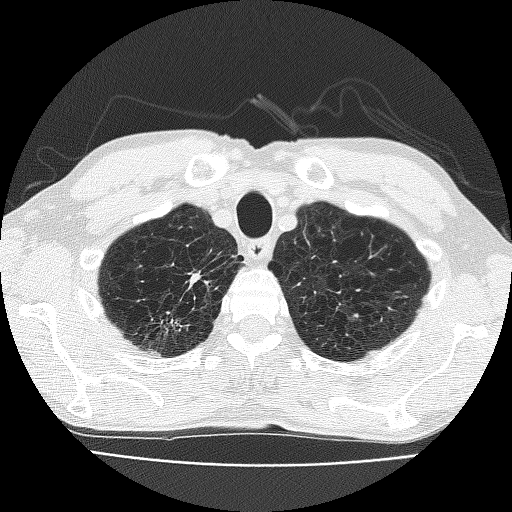
Chest CT (low-dose screening protocol), one axial image, third screening round (two years after baseline), lung window (W 1500 / L -600 HU), 2 mm slice thickness, lung (sharp) reconstruction kernel (FC51), 120 kVp, slice 33 of 185 in the series. Male participant, aged 63 years at enrolment.
• Lesion marked by an expert reader, bounding box <141,255,221,345> (left, top, right, bottom; pixels).
• Screening reader's record for this exam (one nodule recorded; not confirmed to be the boxed lesion): non-calcified nodule or mass ≥4 mm, right upper lobe, 17 × 10 mm, spiculated (stellate) margins, soft tissue attenuation, pre-existing on the prior screen: yes; interval growth: yes.